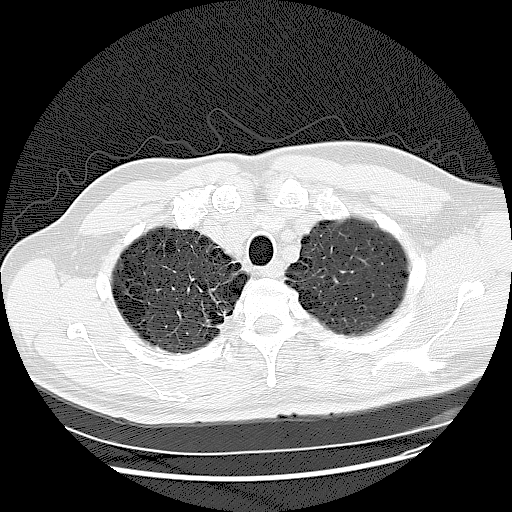
Low-dose screening chest CT, one axial slice. 120 kVp. Lung window (W 1500 / L -600 HU). 512 × 512 image matrix.
Outlined on this slice (manually delineated by an expert):
- lesion 1 (tumor, upper lobe of right lung): box from (x=202, y=310) to (x=227, y=329) px